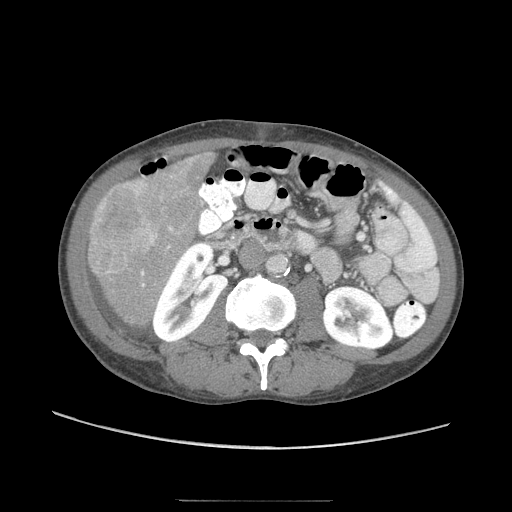
Contrast-enhanced abdominal CT (liver protocol), one axial slice. Slice 16 of 103 in the series (ordered by position). Reconstruction kernel STANDARD. 120 kVp. Soft-tissue window (W 400 / L 40 HU). 2.5 mm slice thickness. 512 × 512 image matrix, field of view 380 × 380 mm. Case-level facts recorded for this patient, not image findings: diagnosis: hepatocellular carcinoma (patient treated with transarterial chemoembolisation; whether this scan precedes or follows treatment is not stated here); TNM stage (as recorded): Stage-IIIA; Child-Pugh class: A; tumour differentiation: moderately differentiated; tumour size: 16 cm.
Structures marked on this image (semi-automatic segmentation, software-assisted and operator-edited):
- liver parenchyma outside the tumour (the mass and vessels are separate outlines, so this box may not span the whole liver): bounding box [x1, y1, x2, y2] px = [88, 152, 214, 328]
- mass: [89, 178, 158, 276]